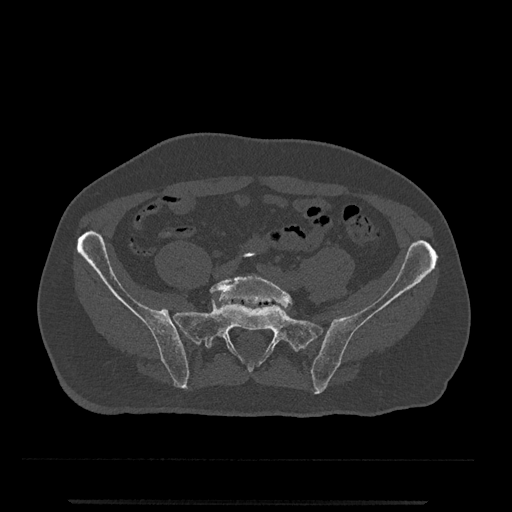
CT including the spine, one axial slice. Slice 30 of 797 in the series (ordered by position). 120 kVp. Bone window (W 1800 / L 400 HU). 0.5 mm slice thickness. 512 × 512 image matrix, field of view 419 × 419 mm. Male patient, age 63 years. Case-level facts recorded for this patient, not image findings: primary cancer: prostate.
Structures marked on this image (semi-automatic segmentation, software-assisted and operator-edited):
- L5 vertebra: bounding box (x1, y1, x2, y2) in pixels: (210, 275, 293, 308)